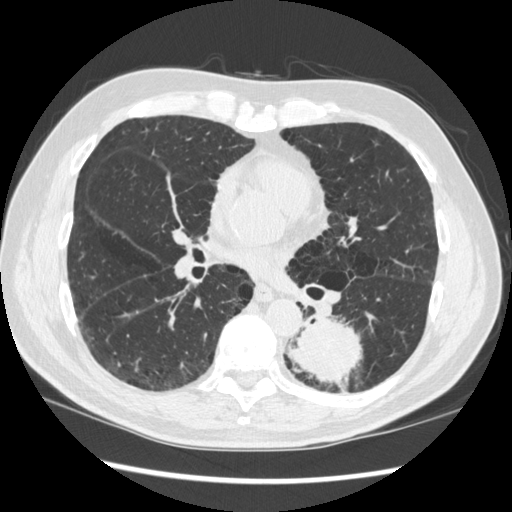
Low-dose screening chest CT, one axial slice. 120 kVp. Lung window (W 1500 / L -600 HU). 1.25 mm slice thickness. 512 × 512 image matrix, field of view 360 × 360 mm.
Structures marked on this image (expert manual segmentation):
- lesion 1 (tumor, lower lobe of left lung): bounding box [x1, y1, x2, y2] px = [289, 319, 362, 384]